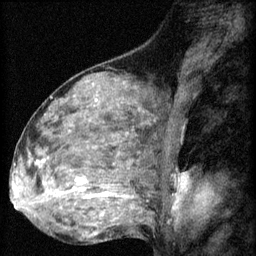
Breast MRI (dynamic contrast-enhanced), one sagittal slice; position 37 of 60 along the scan axis; 3 images stored at this slice position (order not interpretable as contrast timing); 1.5 T; TE 4.2 ms, TR 8.2 ms; 2 mm slice thickness; 256 × 256 image matrix, field of view 180 × 180 mm. Female patient, age 48 years.
Annotated regions visible in this slice (semi-automatic segmentation, software-assisted and operator-edited):
- analysis volume of interest (the breast-tissue region the enhancement analysis was run in; not a lesion): bounding box (x1, y1, x2, y2) in pixels: (48, 160, 125, 217)
- tumour enhancement mask (voxels above the 70 % enhancement threshold inside the analysis volume of interest): (72, 178, 85, 193)